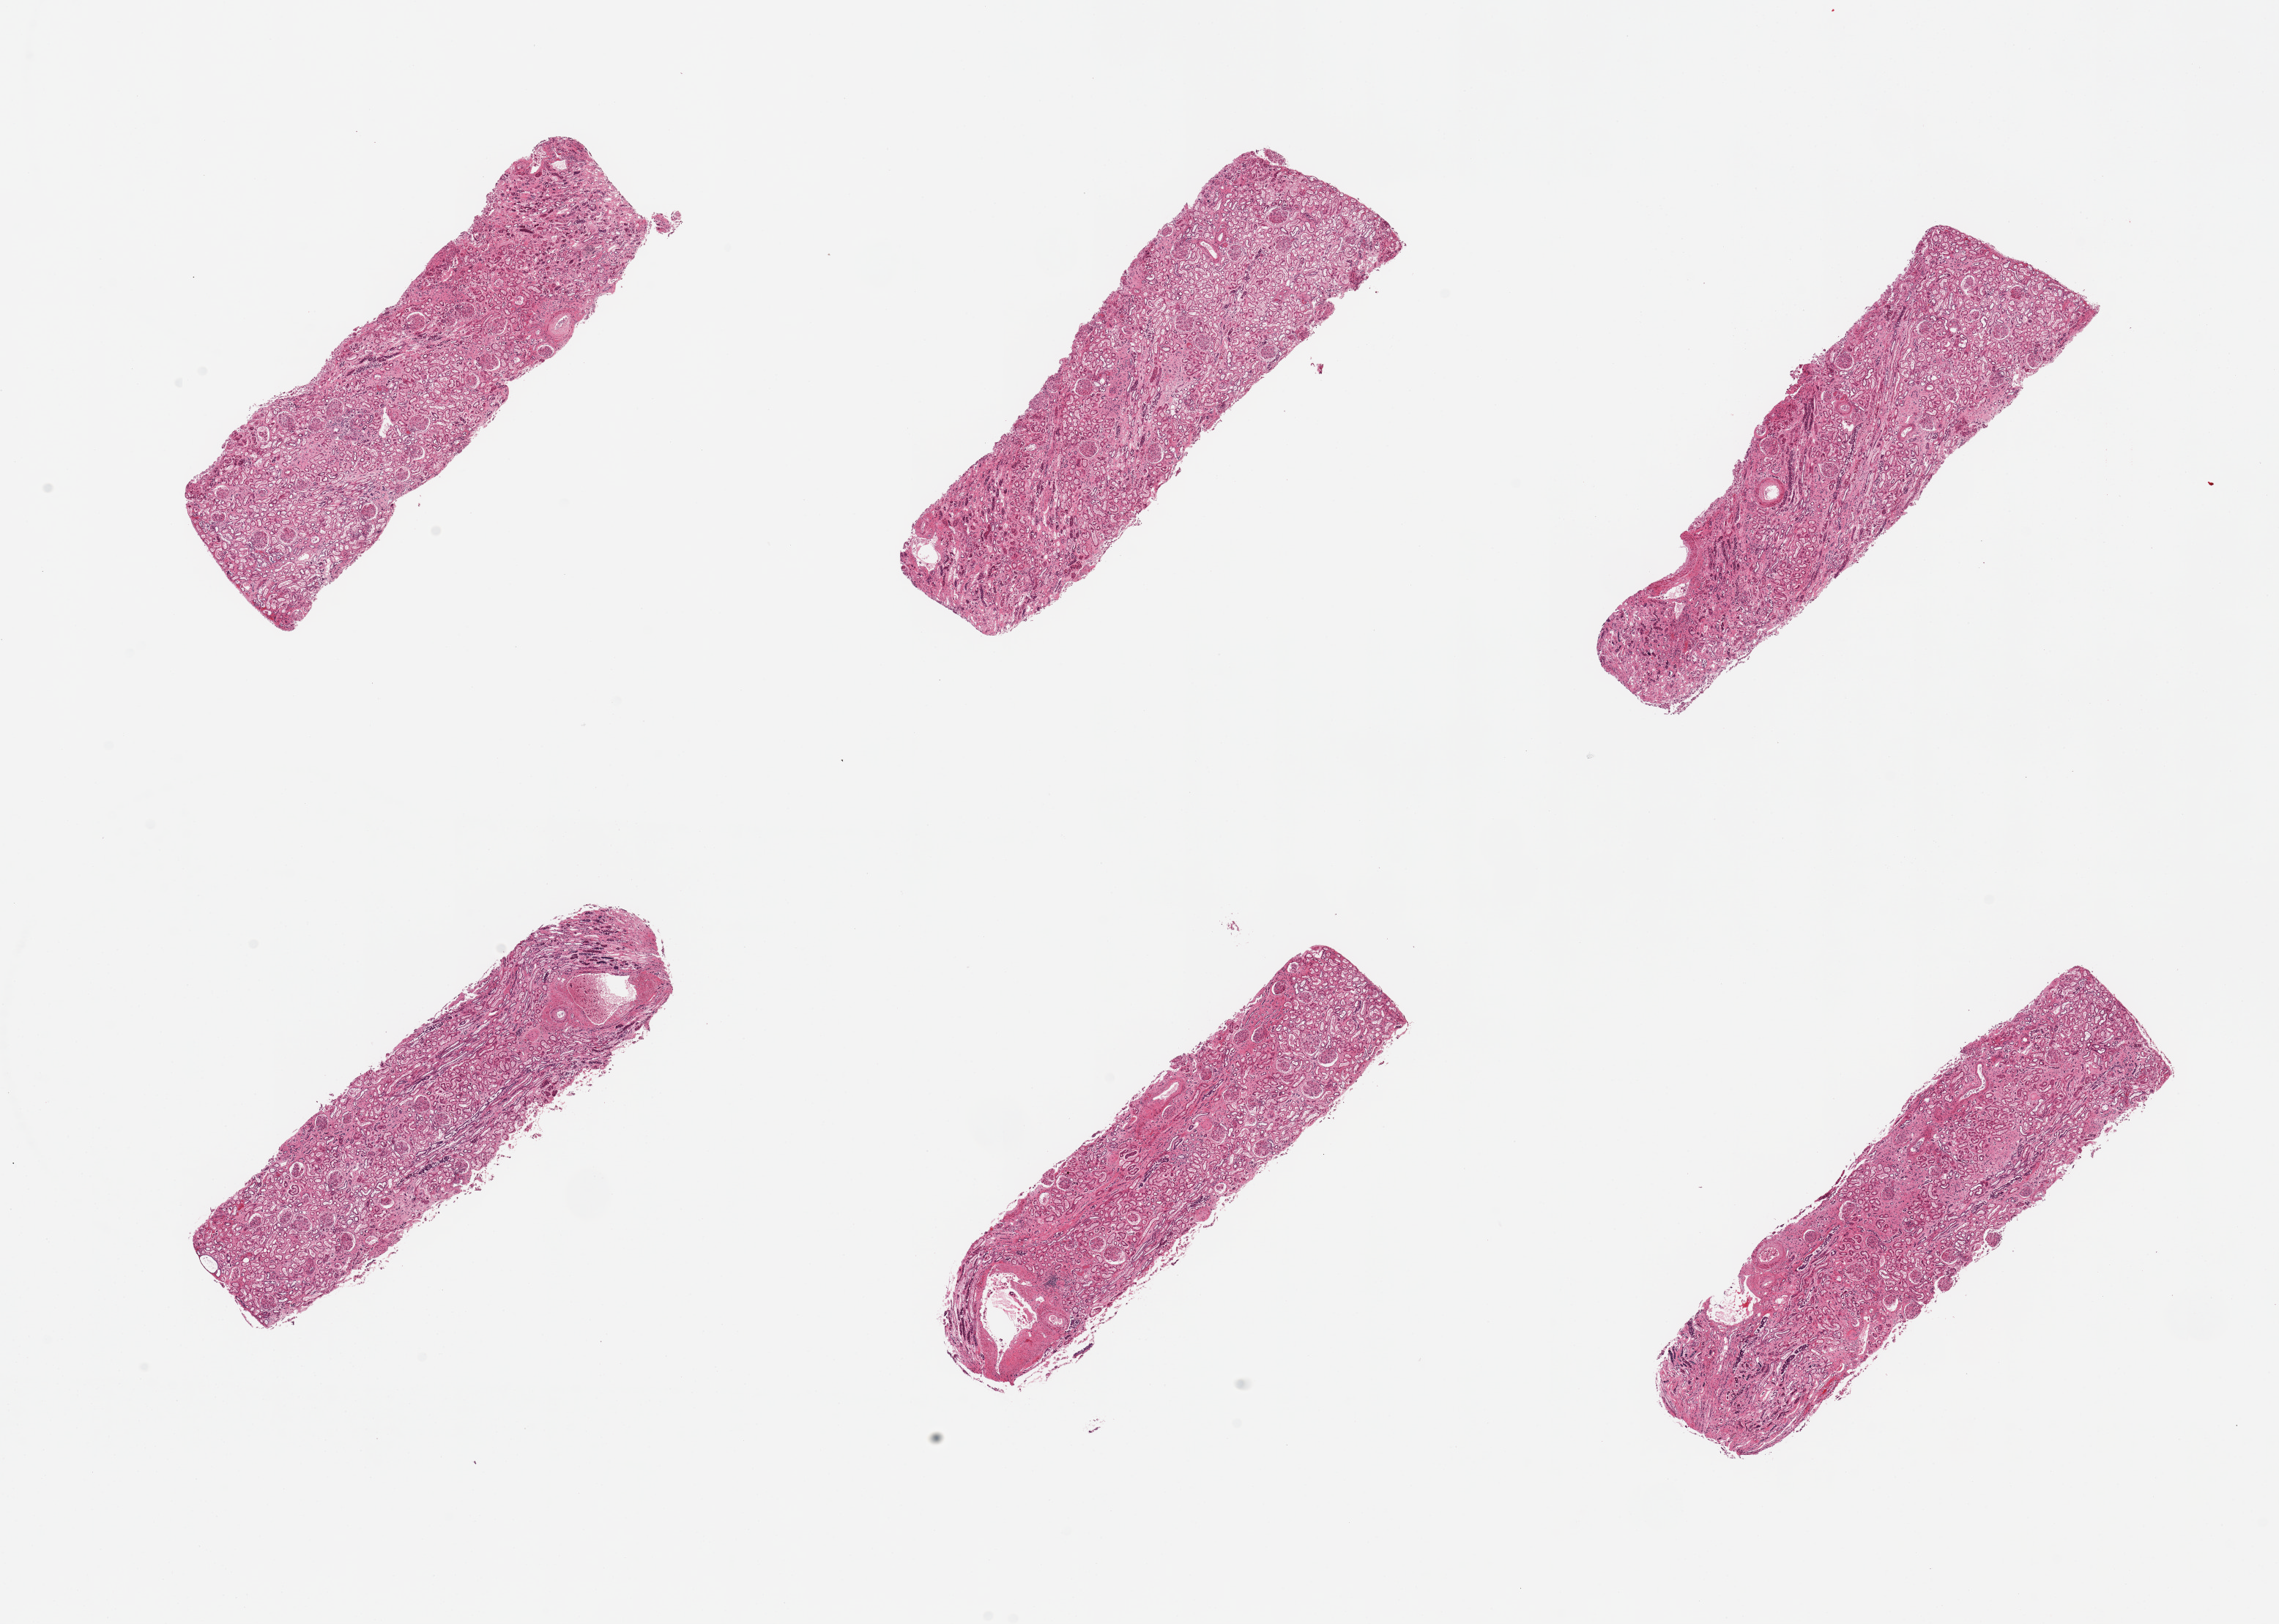
H&E whole-slide image — shown as a low-resolution overview of the whole scanned area (about 24.6 x 17.5 mm); PAXgene-fixed, paraffin-embedded tissue; target tissue: renal cortex; tissue donor sample. Donor: male.
Review note (as recorded): 6 pieces, glomeruli present in all sections, some areas approach score 2 for autolysis, better preserved than typical.